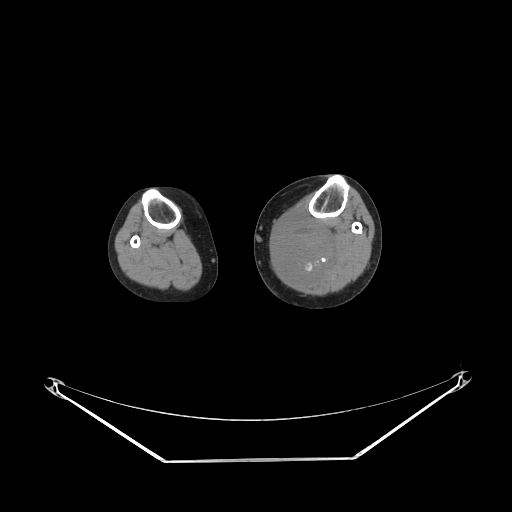
CT of an extremity soft-tissue mass (from a PET/CT study), one axial slice. Position 151 of 223 along the scan axis. 140 kVp. Soft-tissue window (W 400 / L 40 HU). 3.75 mm slice thickness. 512 × 512 image matrix. Female patient. Case-level facts recorded for this patient, not image findings: histological type: extraskeletal high grade osteogenic sarcoma; grade: high; site of the primary tumour: left calf.
Annotated regions visible in this slice (expert contour drawn on MRI and transferred to this co-registered scan by the dataset authors):
- gross tumour volume (mass): bounding box [x1, y1, x2, y2] px = [272, 217, 337, 280]